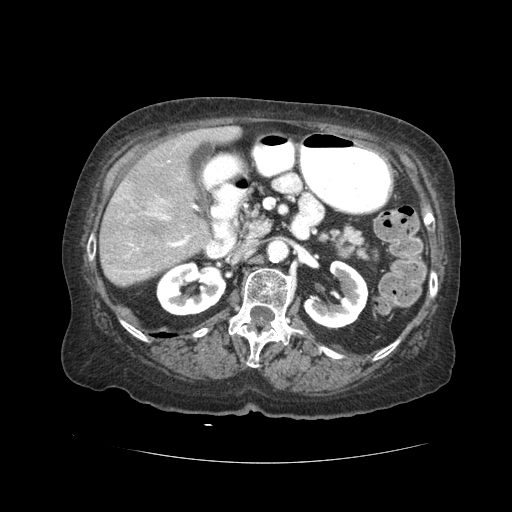
Contrast-enhanced abdominal CT (liver protocol), one axial slice. 120 kVp. Soft-tissue window (W 400 / L 40 HU). 512 × 512 image matrix. Case-level facts recorded for this patient, not image findings: diagnosis: hepatocellular carcinoma (patient treated with transarterial chemoembolisation; whether this scan precedes or follows treatment is not stated here); TNM stage (as recorded): Stage-I; Child-Pugh class: A; tumour nodularity: uninodular.
Annotated regions visible in this slice (semi-automatic segmentation, software-assisted and operator-edited):
- liver parenchyma outside the tumour (the mass and vessels are separate outlines, so this box may not span the whole liver): bounding box (x1, y1, x2, y2) in pixels: (100, 126, 241, 286)
- mass: (145, 196, 177, 221)
- liver vessels: (127, 205, 198, 273)